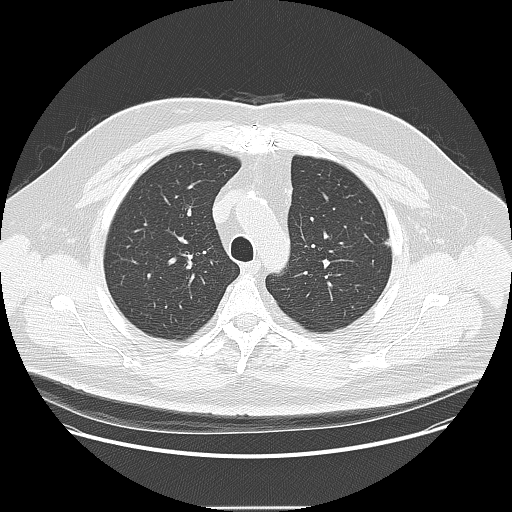
Low-dose screening chest CT, one axial slice; slice 114 of 157 in the series (ordered by position); reconstruction kernel LUNG; 120 kVp; lung window (W 1500 / L -600 HU); 512 × 512 image matrix, field of view 410 × 410 mm.
Structures marked on this image (manually delineated by an expert):
- lesion 1 (tumor, upper lobe of left lung): bounding box (x1, y1, x2, y2) in pixels: (384, 238, 391, 247)